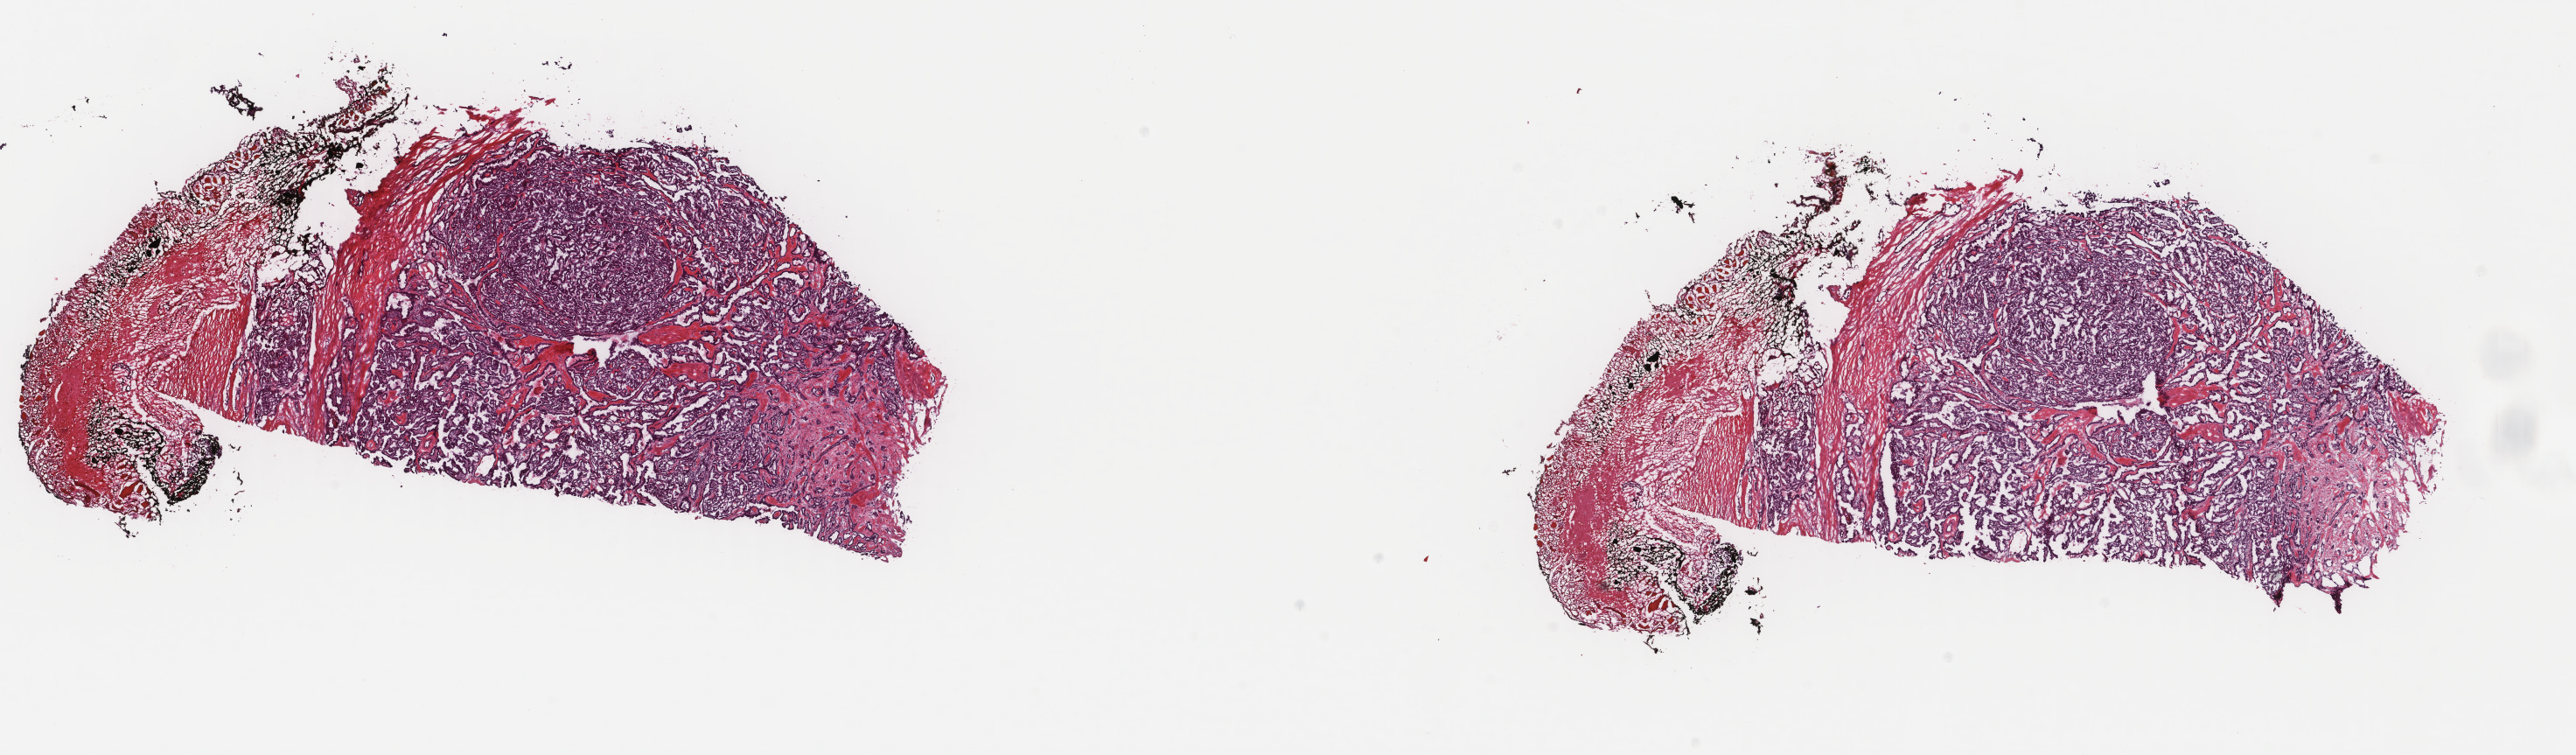
Digitized Hematoxylin and eosin (H&E) stained tissue section (whole slide), shown as a low-resolution overview of the whole scanned area (about 23.4 x 6.8 mm, slide scanned at 40x); frozen section from the top of the tissue portion; thyroid, primary tumour sample. Female, age 72 years at initial diagnosis. Composition of this section per pathologist review: tumour cells 70%, tumour nuclei 90%, normal cells 10%, stromal cells 20%, necrosis 0%. Inflammatory infiltration, as recorded: lymphocyte infiltration 1%, monocyte infiltration 0%, neutrophil infiltration 0%.
TNM: T1b NX MX. AJCC pathologic stage: I (7th edition). Histologic diagnosis: Papillary adenocarcinoma, NOS (thyroid gland).